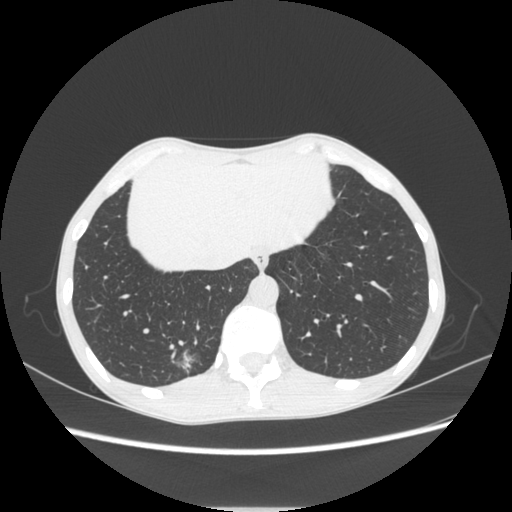
Chest CT, one axial slice; reconstruction kernel STANDARD; lung window (W 1500 / L -600 HU); 1.25 mm slice thickness; 512 × 512 image matrix. Patient: female, 51 years. Case-level facts recorded for this patient, not image findings: clinical TNM (as recorded): T1c N0 M0.
Annotated regions visible in this slice (rectangle marked by the reading radiologist):
- lung tumour (recorded histology: adenocarcinoma): bounding box <160,336,208,382> (left, top, right, bottom; pixels)